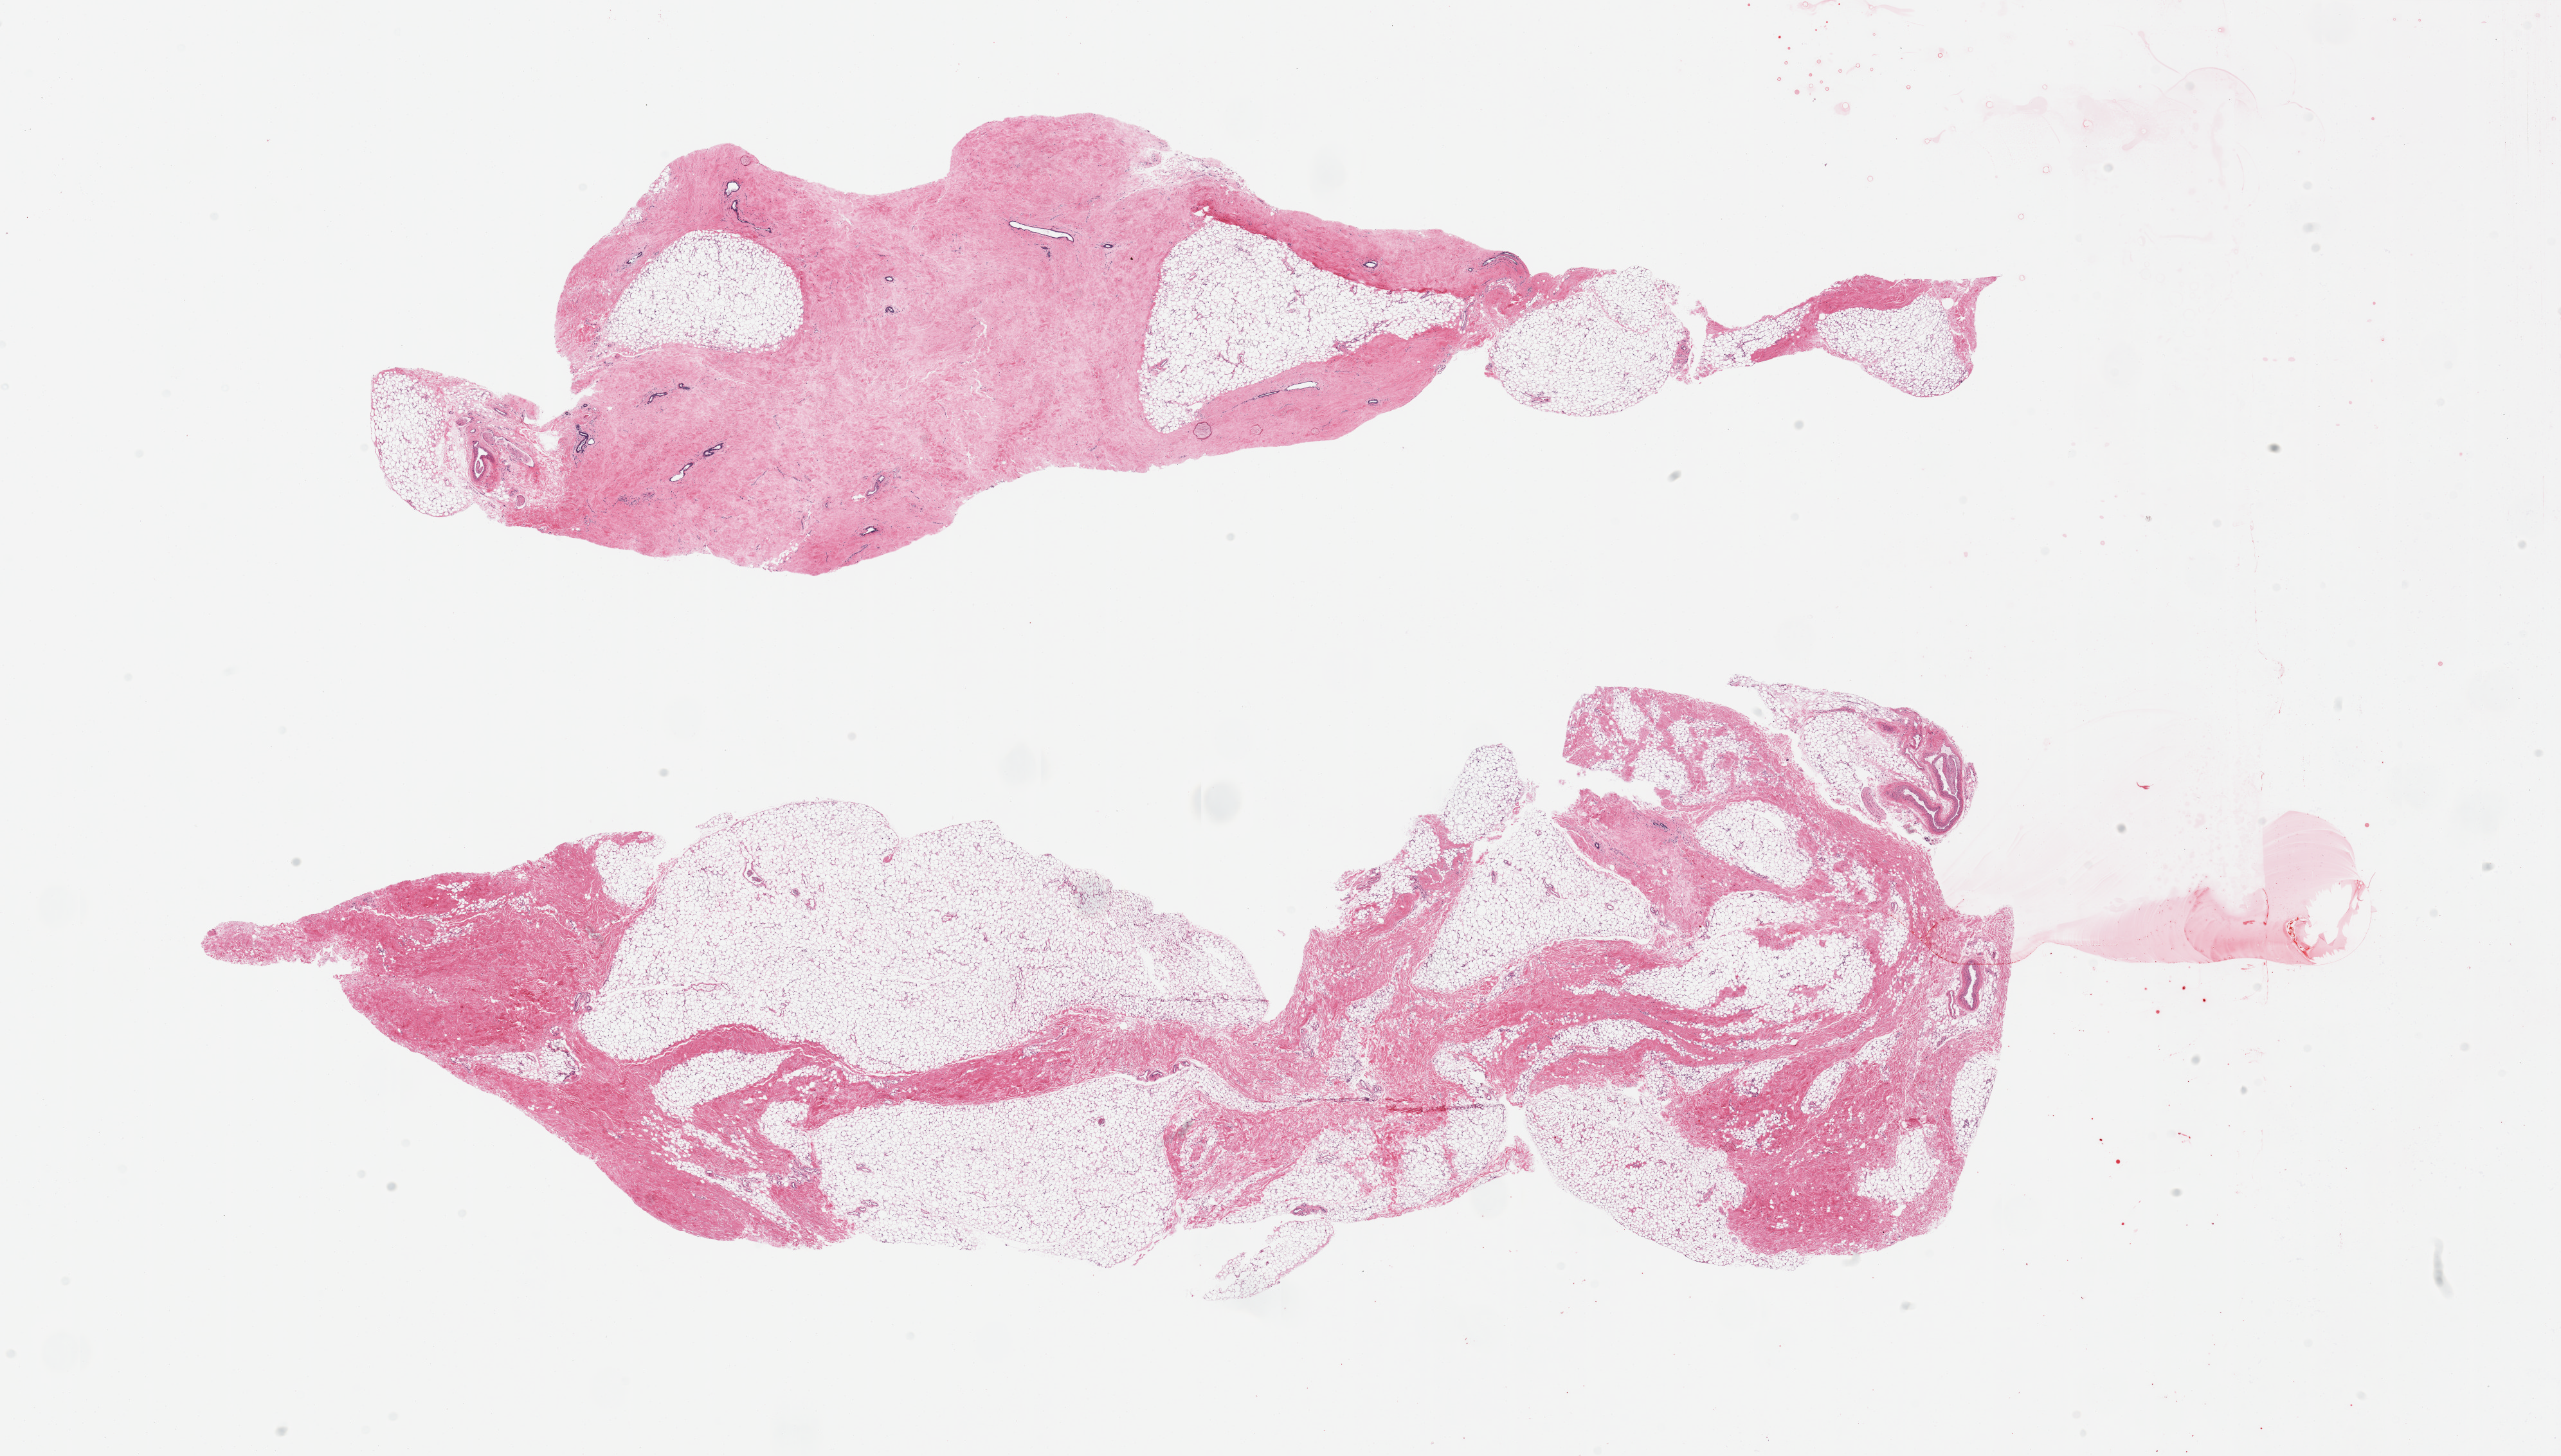
Haematoxylin and eosin whole-slide image, brightfield, low-resolution overview of the scanned area, about 31.5 x 17.9 mm (slide scanned at 20x); PAXgene-fixed, paraffin-embedded tissue; target tissue: breast; tissue donor sample. Male donor.
* review note (as recorded): 2 pieces, gynecomastoid stromal hyperplasia, few ductal elements present